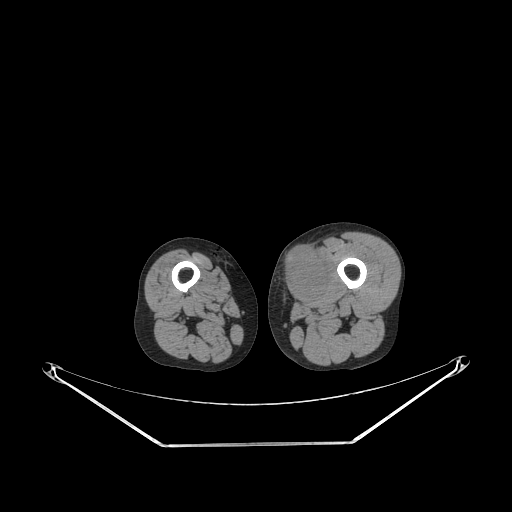
CT of an extremity soft-tissue mass (from a PET/CT study), one axial slice; 140 kVp; soft-tissue window (W 400 / L 40 HU); 3.75 mm slice thickness; 512 × 512 image matrix, field of view 500 × 500 mm. Male patient. Case-level facts recorded for this patient, not image findings: histological type: pleiomorphic leiomyosarcoma; grade: high; site of the primary tumour: left thigh.
Annotated regions visible in this slice (expert contour drawn on MRI and transferred to this co-registered scan by the dataset authors):
- gross tumour volume including surrounding oedema: box from (x=281, y=247) to (x=330, y=300) px
- gross tumour volume (mass): (x=281, y=249)–(x=325, y=300)